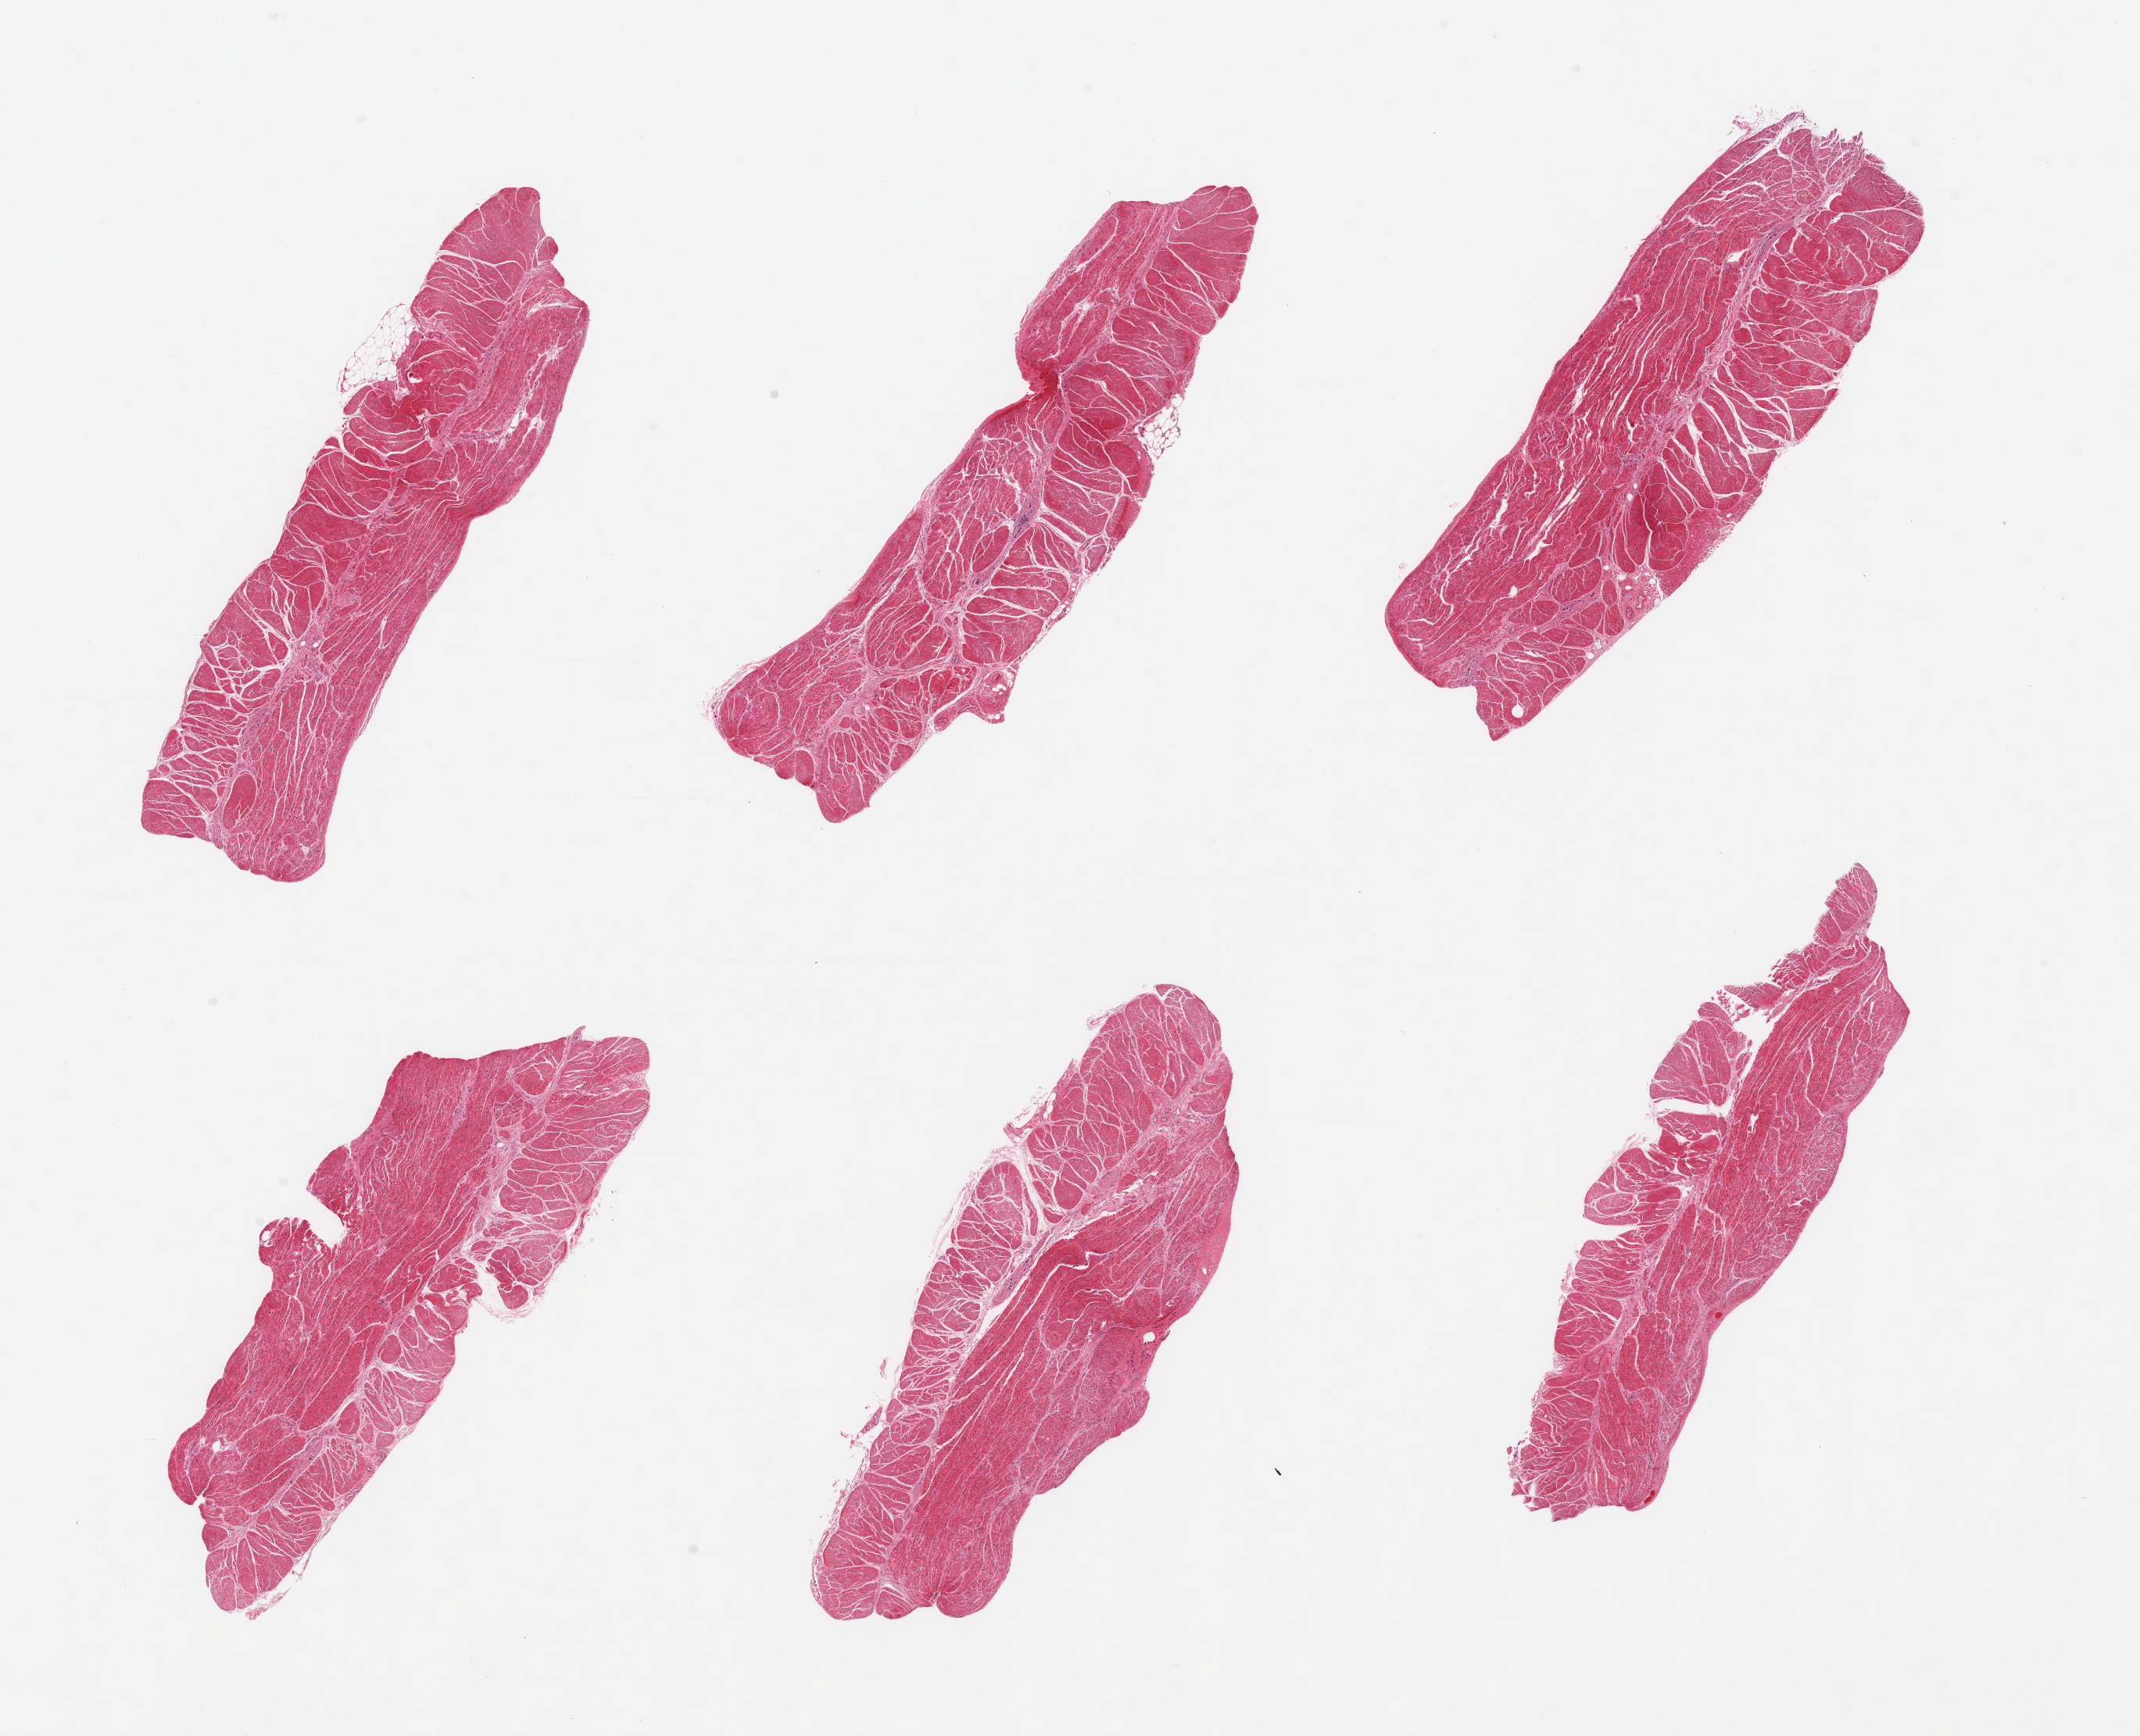
Whole-slide image, hematoxylin and eosin (H&E) stain — whole scanned area (about 21.7 x 17.6 mm) shown as a low-resolution overview. PAXgene-fixed, paraffin-embedded tissue. Target tissue: esophageal muscle. Donor tissue sample.
Pathologist's review note for this sample: 6 pieces, confirmed target muscularis.